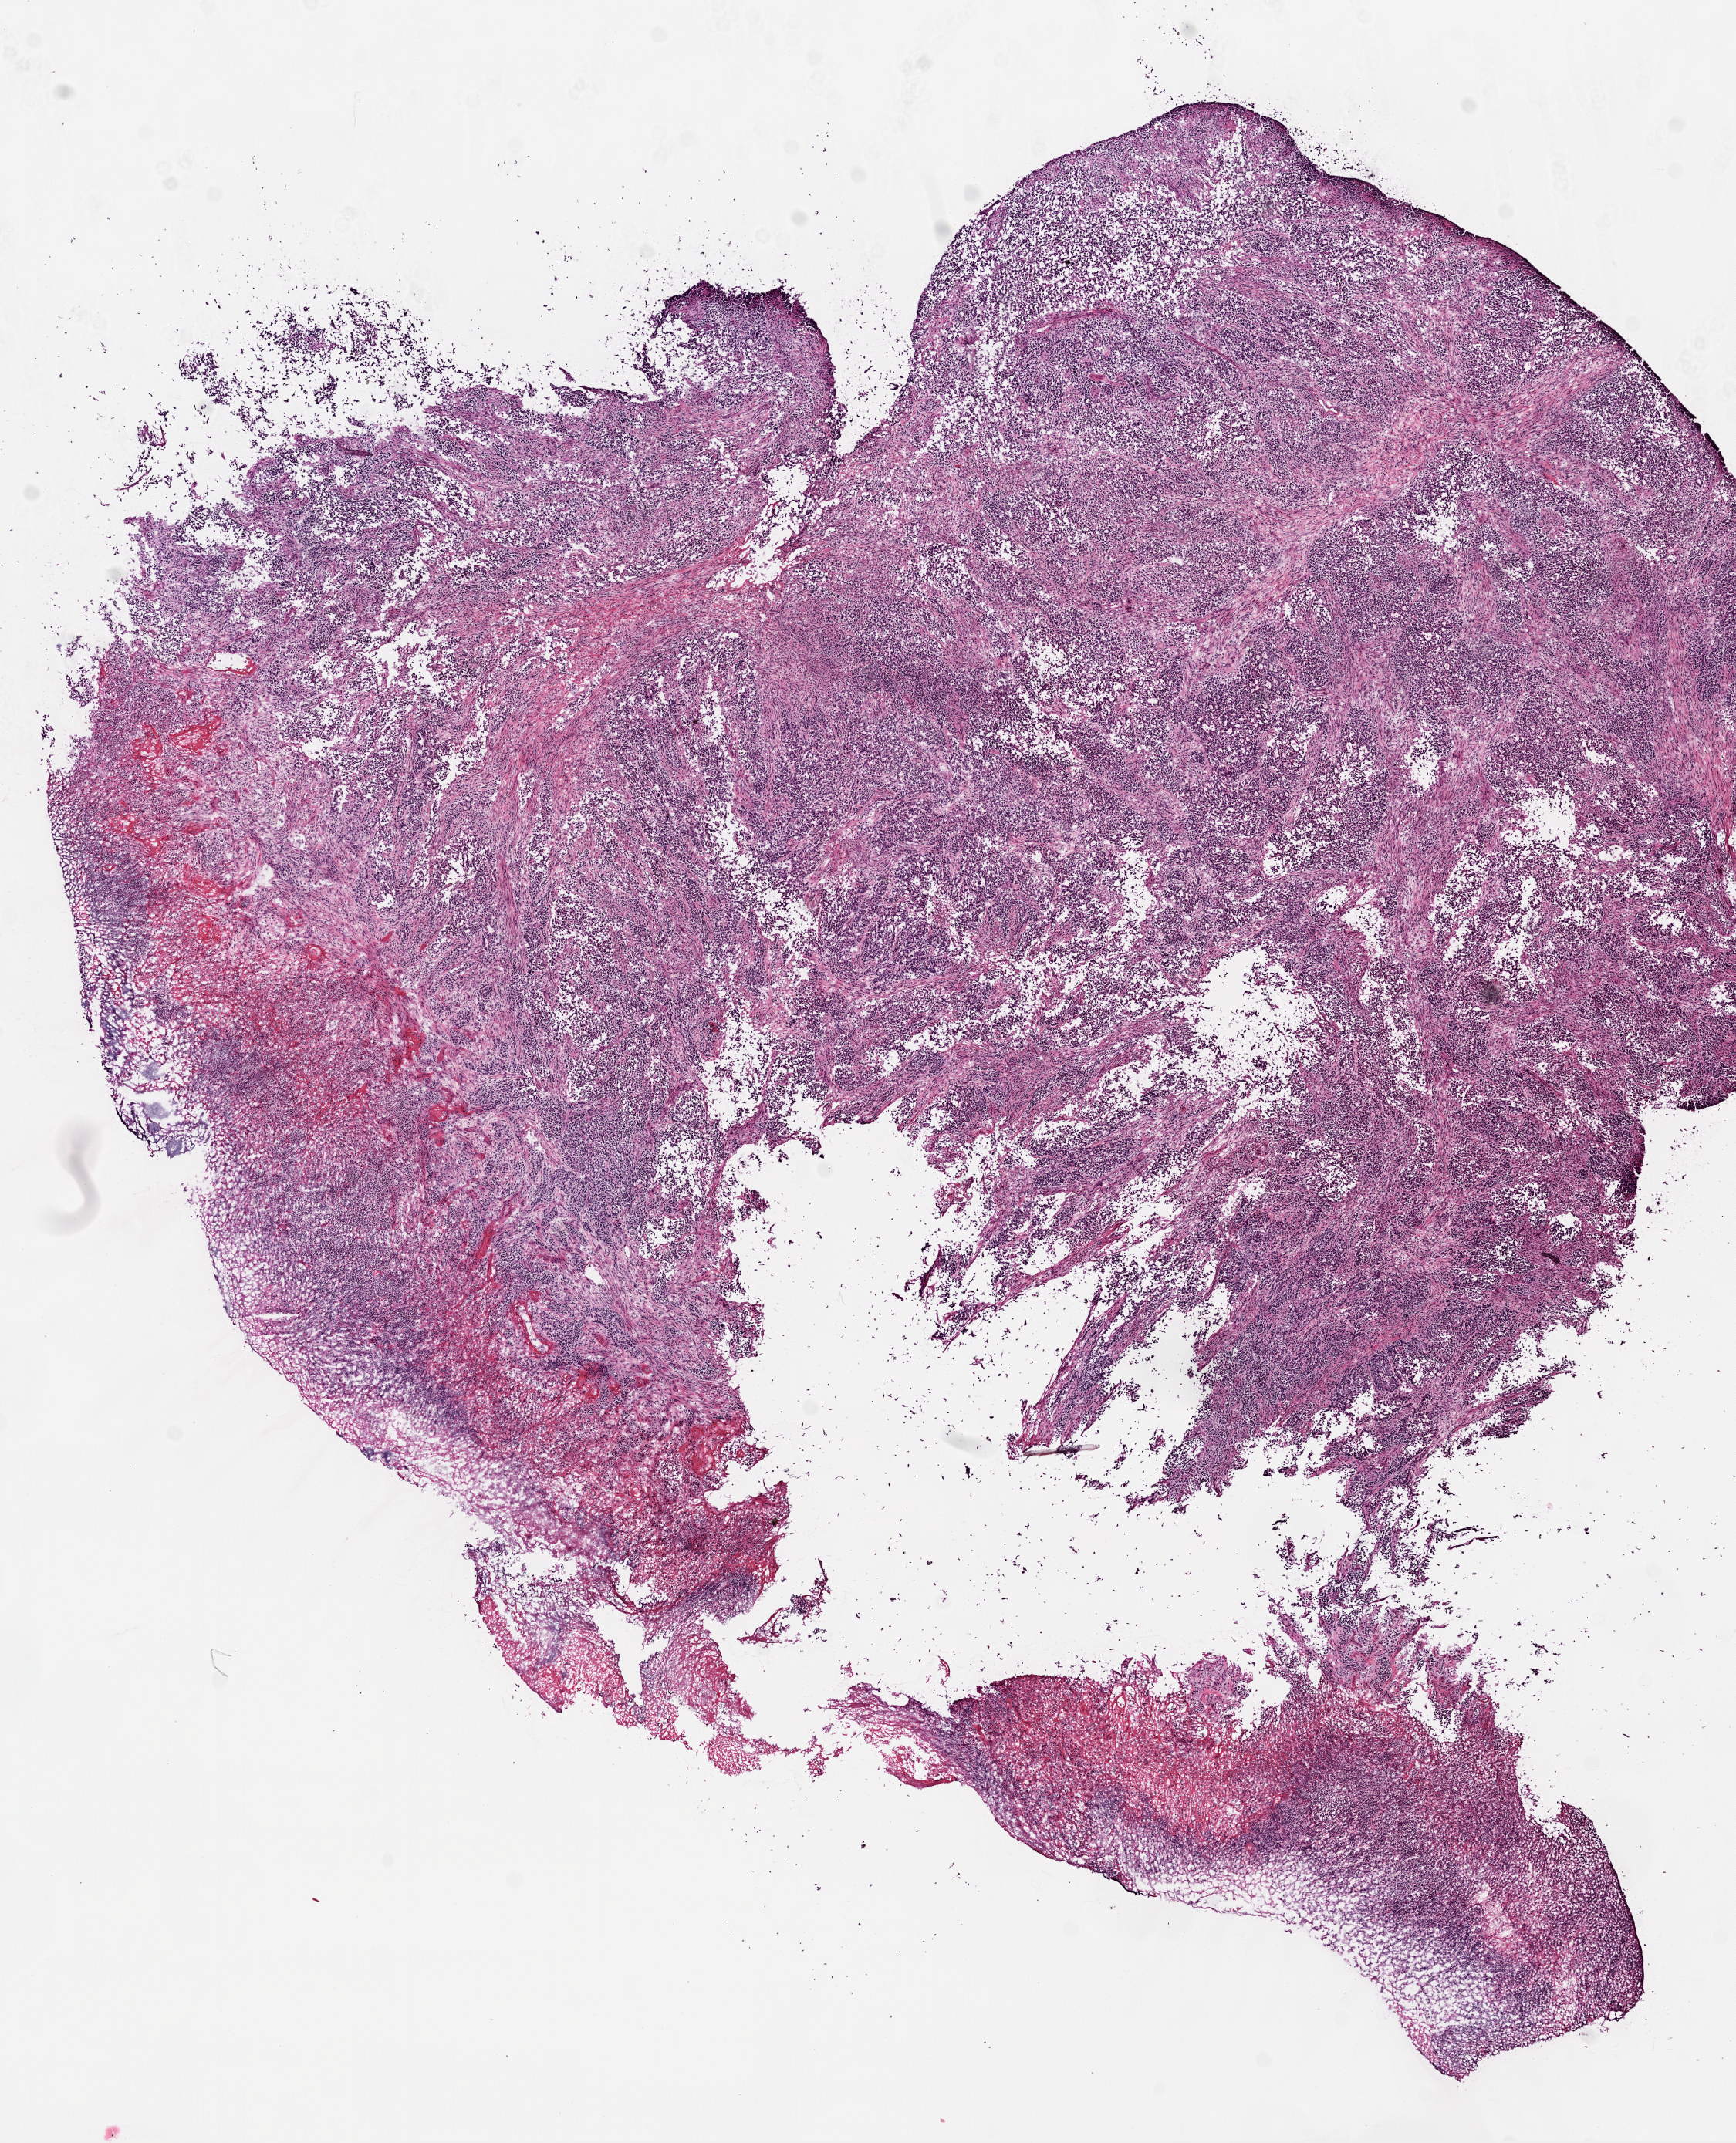
Digitized Hematoxylin and eosin (H&E) stained tissue section (whole slide), whole scanned area (about 9.0 x 11.1 mm, acquisition: 20x scan) shown as a low-resolution overview, frozen section from the top of the tissue portion, stomach, primary tumour sample. Male, age 62 years at initial diagnosis.
Diagnosis: Carcinoma, diffuse type (body of stomach).